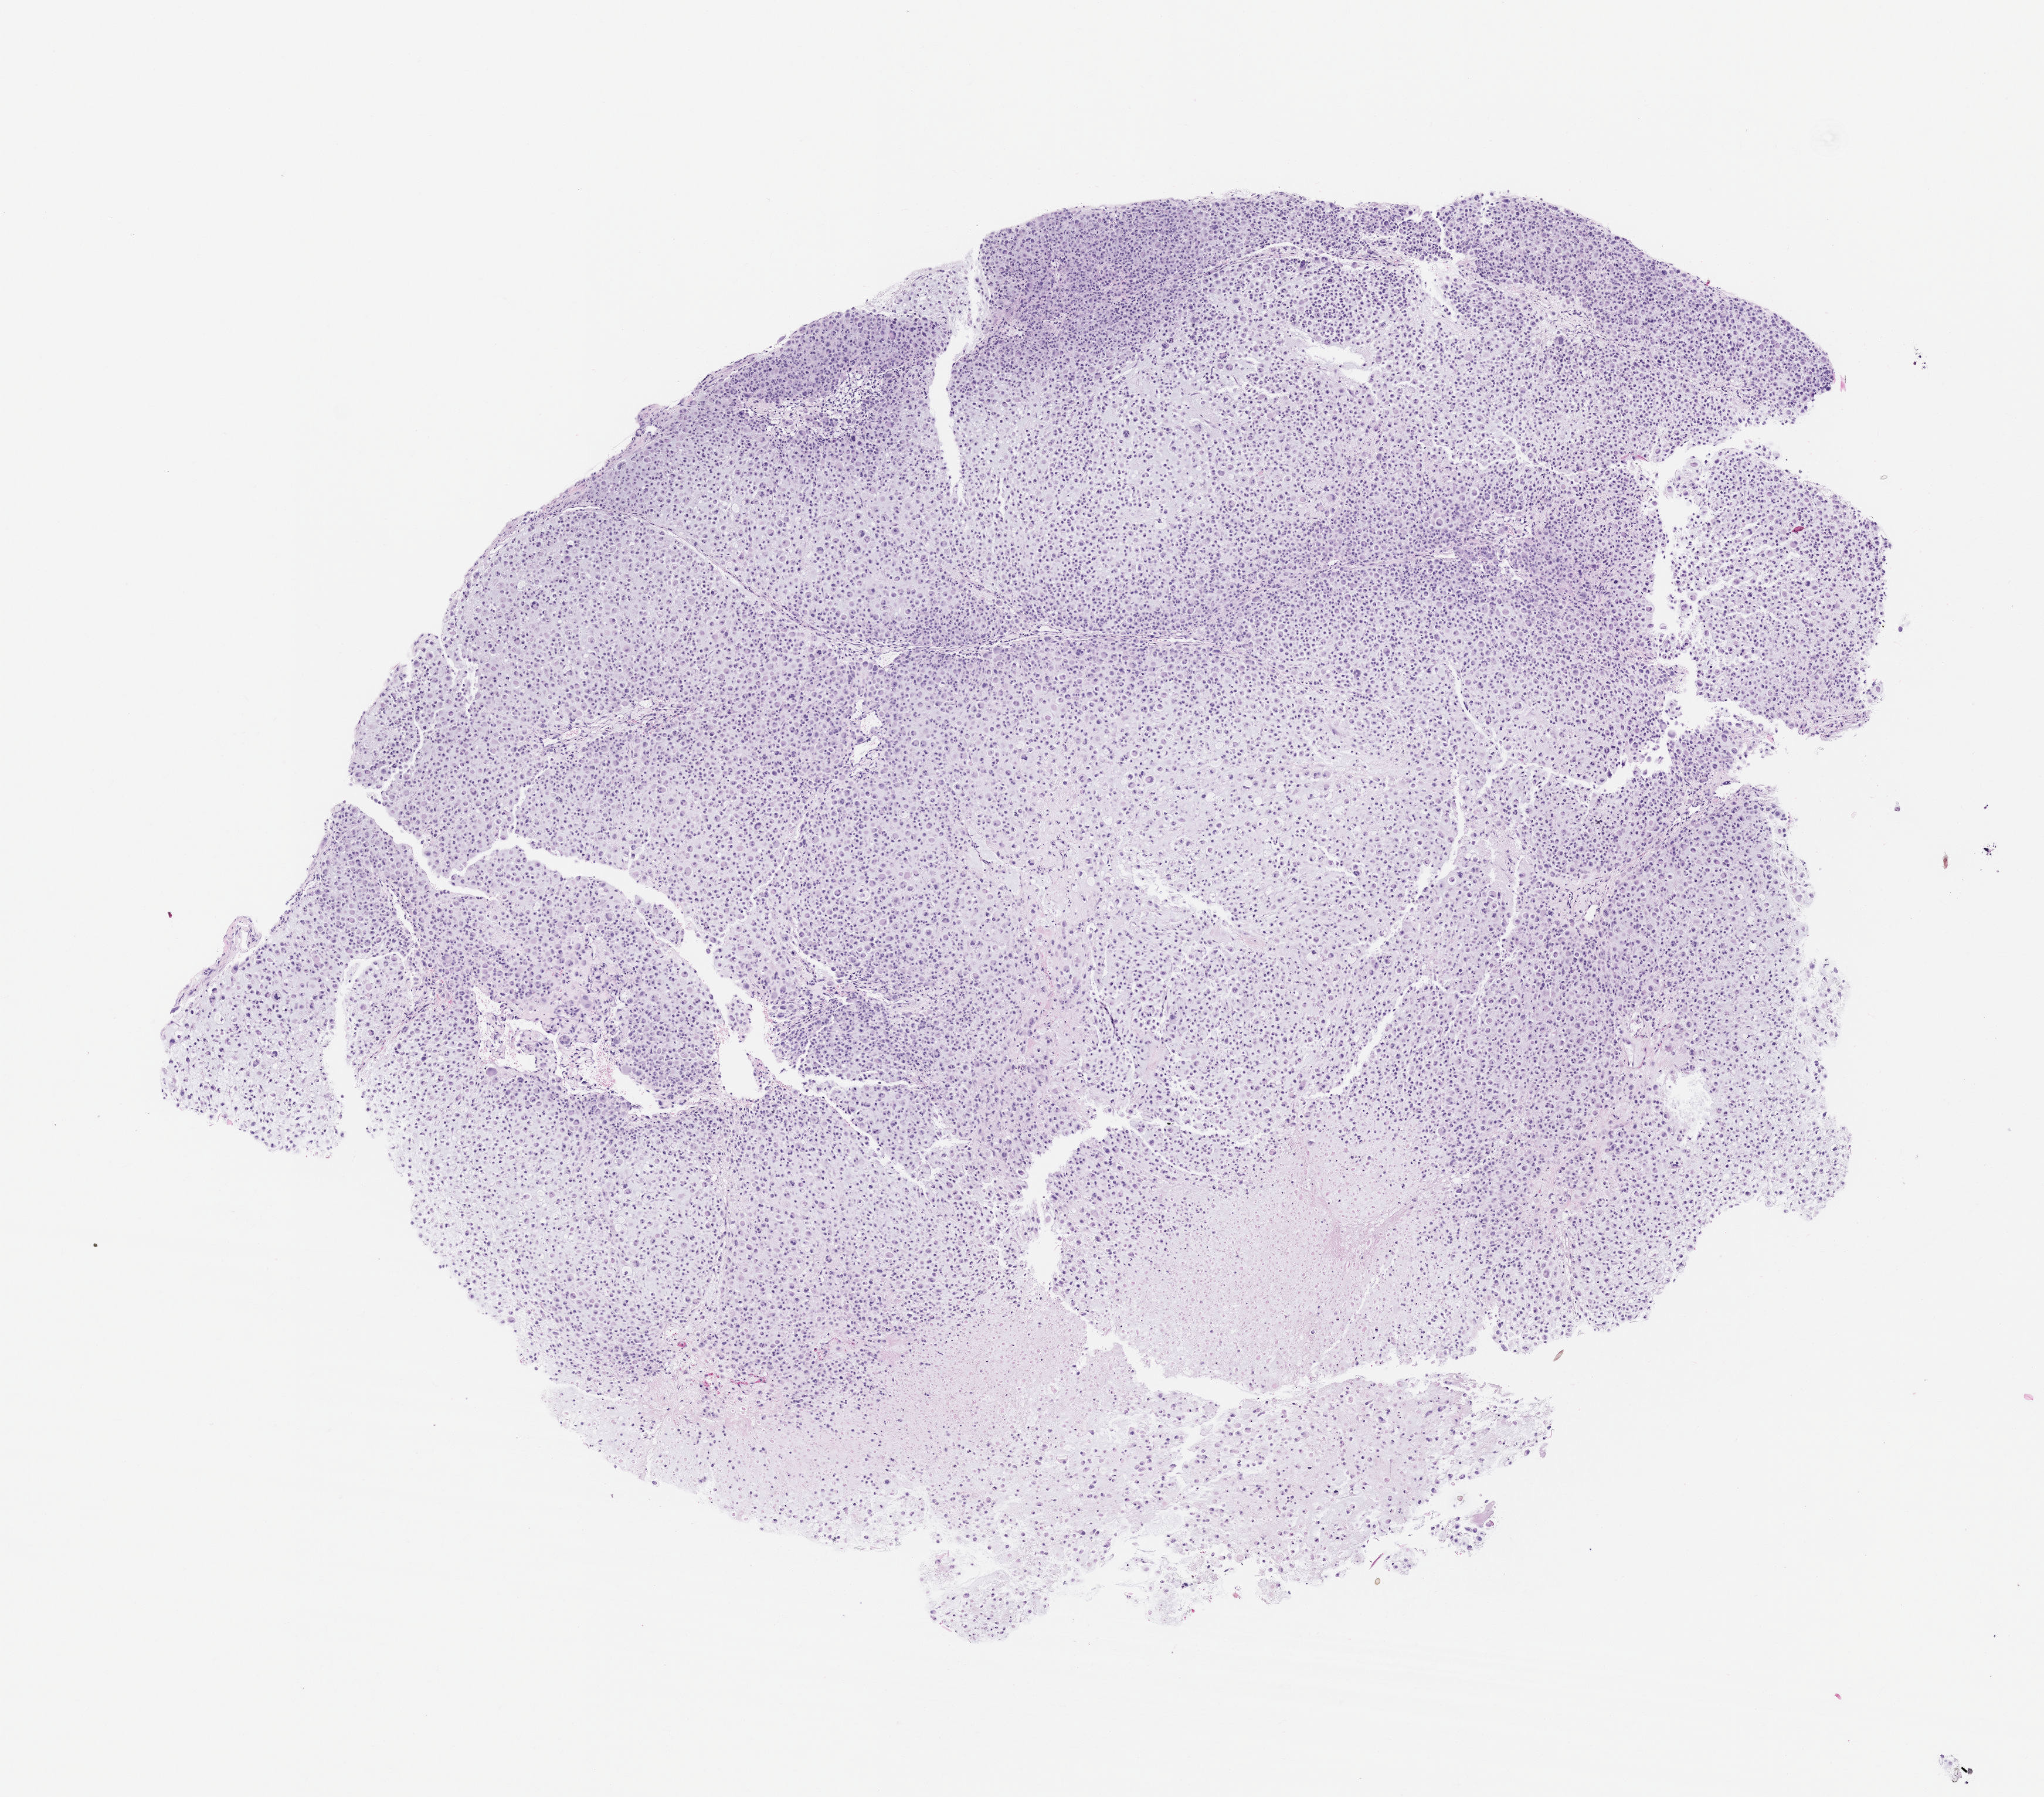
Whole-slide image, haematoxylin and eosin: patient-derived xenograft (human tumor grown in a mouse), passage 2 — shown as a low-resolution overview of the whole scanned area (about 7.0 x 6.2 mm), formalin-fixed, paraffin-embedded (FFPE) tissue, tumor site category: musculoskeletal.
* originating patient diagnosis: Chondrosarcoma